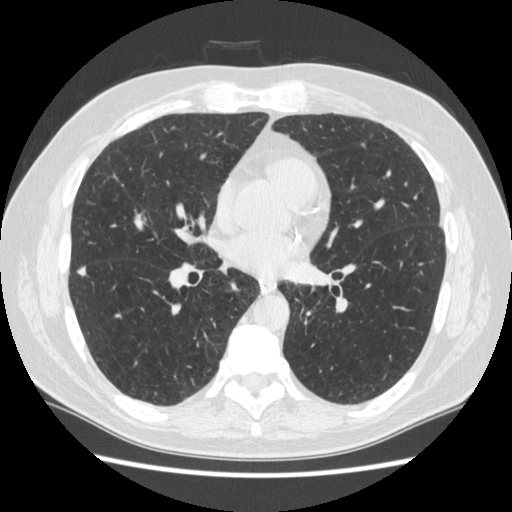
Low-dose screening chest CT, one axial slice. Slice 126 of 267 in the series (ordered by position). Reconstruction kernel STANDARD. Lung window (W 1500 / L -600 HU). 1.25 mm slice thickness. 512 × 512 image matrix, field of view 360 × 360 mm.
Outlined on this slice (manually delineated by an expert):
- lesion 2 (nodule, lower lobe of right lung): bounding box (x1, y1, x2, y2) in pixels: (78, 267, 86, 276)